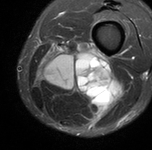
MRI of an extremity soft-tissue mass, one axial slice. STIR. MR volume resampled by the dataset authors to the PET/CT grid (not the native acquisition matrix). 3.27 mm slice thickness. 152 × 150 image matrix. Male patient. From the clinical record (not read from this slice): histological type: undifferentiated pleomorphic liposarcoma; grade: high; site of the primary tumour: left thigh.
Outlined on this slice (expert contour drawn on MRI and transferred to this co-registered scan by the dataset authors):
- gross tumour volume including surrounding oedema: bounding box [x1, y1, x2, y2] px = [36, 41, 119, 122]
- gross tumour volume (mass): [73, 62, 108, 97]